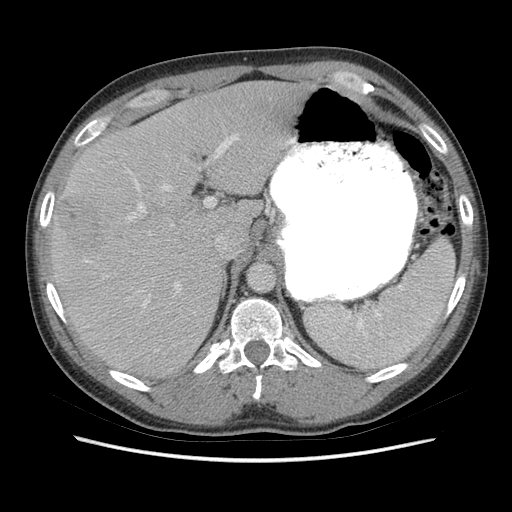
Contrast-enhanced abdominal CT (liver protocol), one axial slice; position 48 of 73 along the scan axis; 140 kVp; soft-tissue window (W 400 / L 40 HU); 512 × 512 image matrix, field of view 360 × 360 mm. From the clinical record (not read from this slice): diagnosis: hepatocellular carcinoma (patient treated with transarterial chemoembolisation; whether this scan precedes or follows treatment is not stated here); TNM stage (as recorded): Stage-IIIA; Child-Pugh class: A; tumour size: 6.6 cm.
Structures marked on this image (semi-automatic segmentation, software-assisted and operator-edited):
- liver parenchyma outside the tumour (the mass and vessels are separate outlines, so this box may not span the whole liver): box from (x=50, y=80) to (x=311, y=378) px
- mass: (x=56, y=196)–(x=104, y=254)
- liver vessels: (x=85, y=135)–(x=238, y=307)